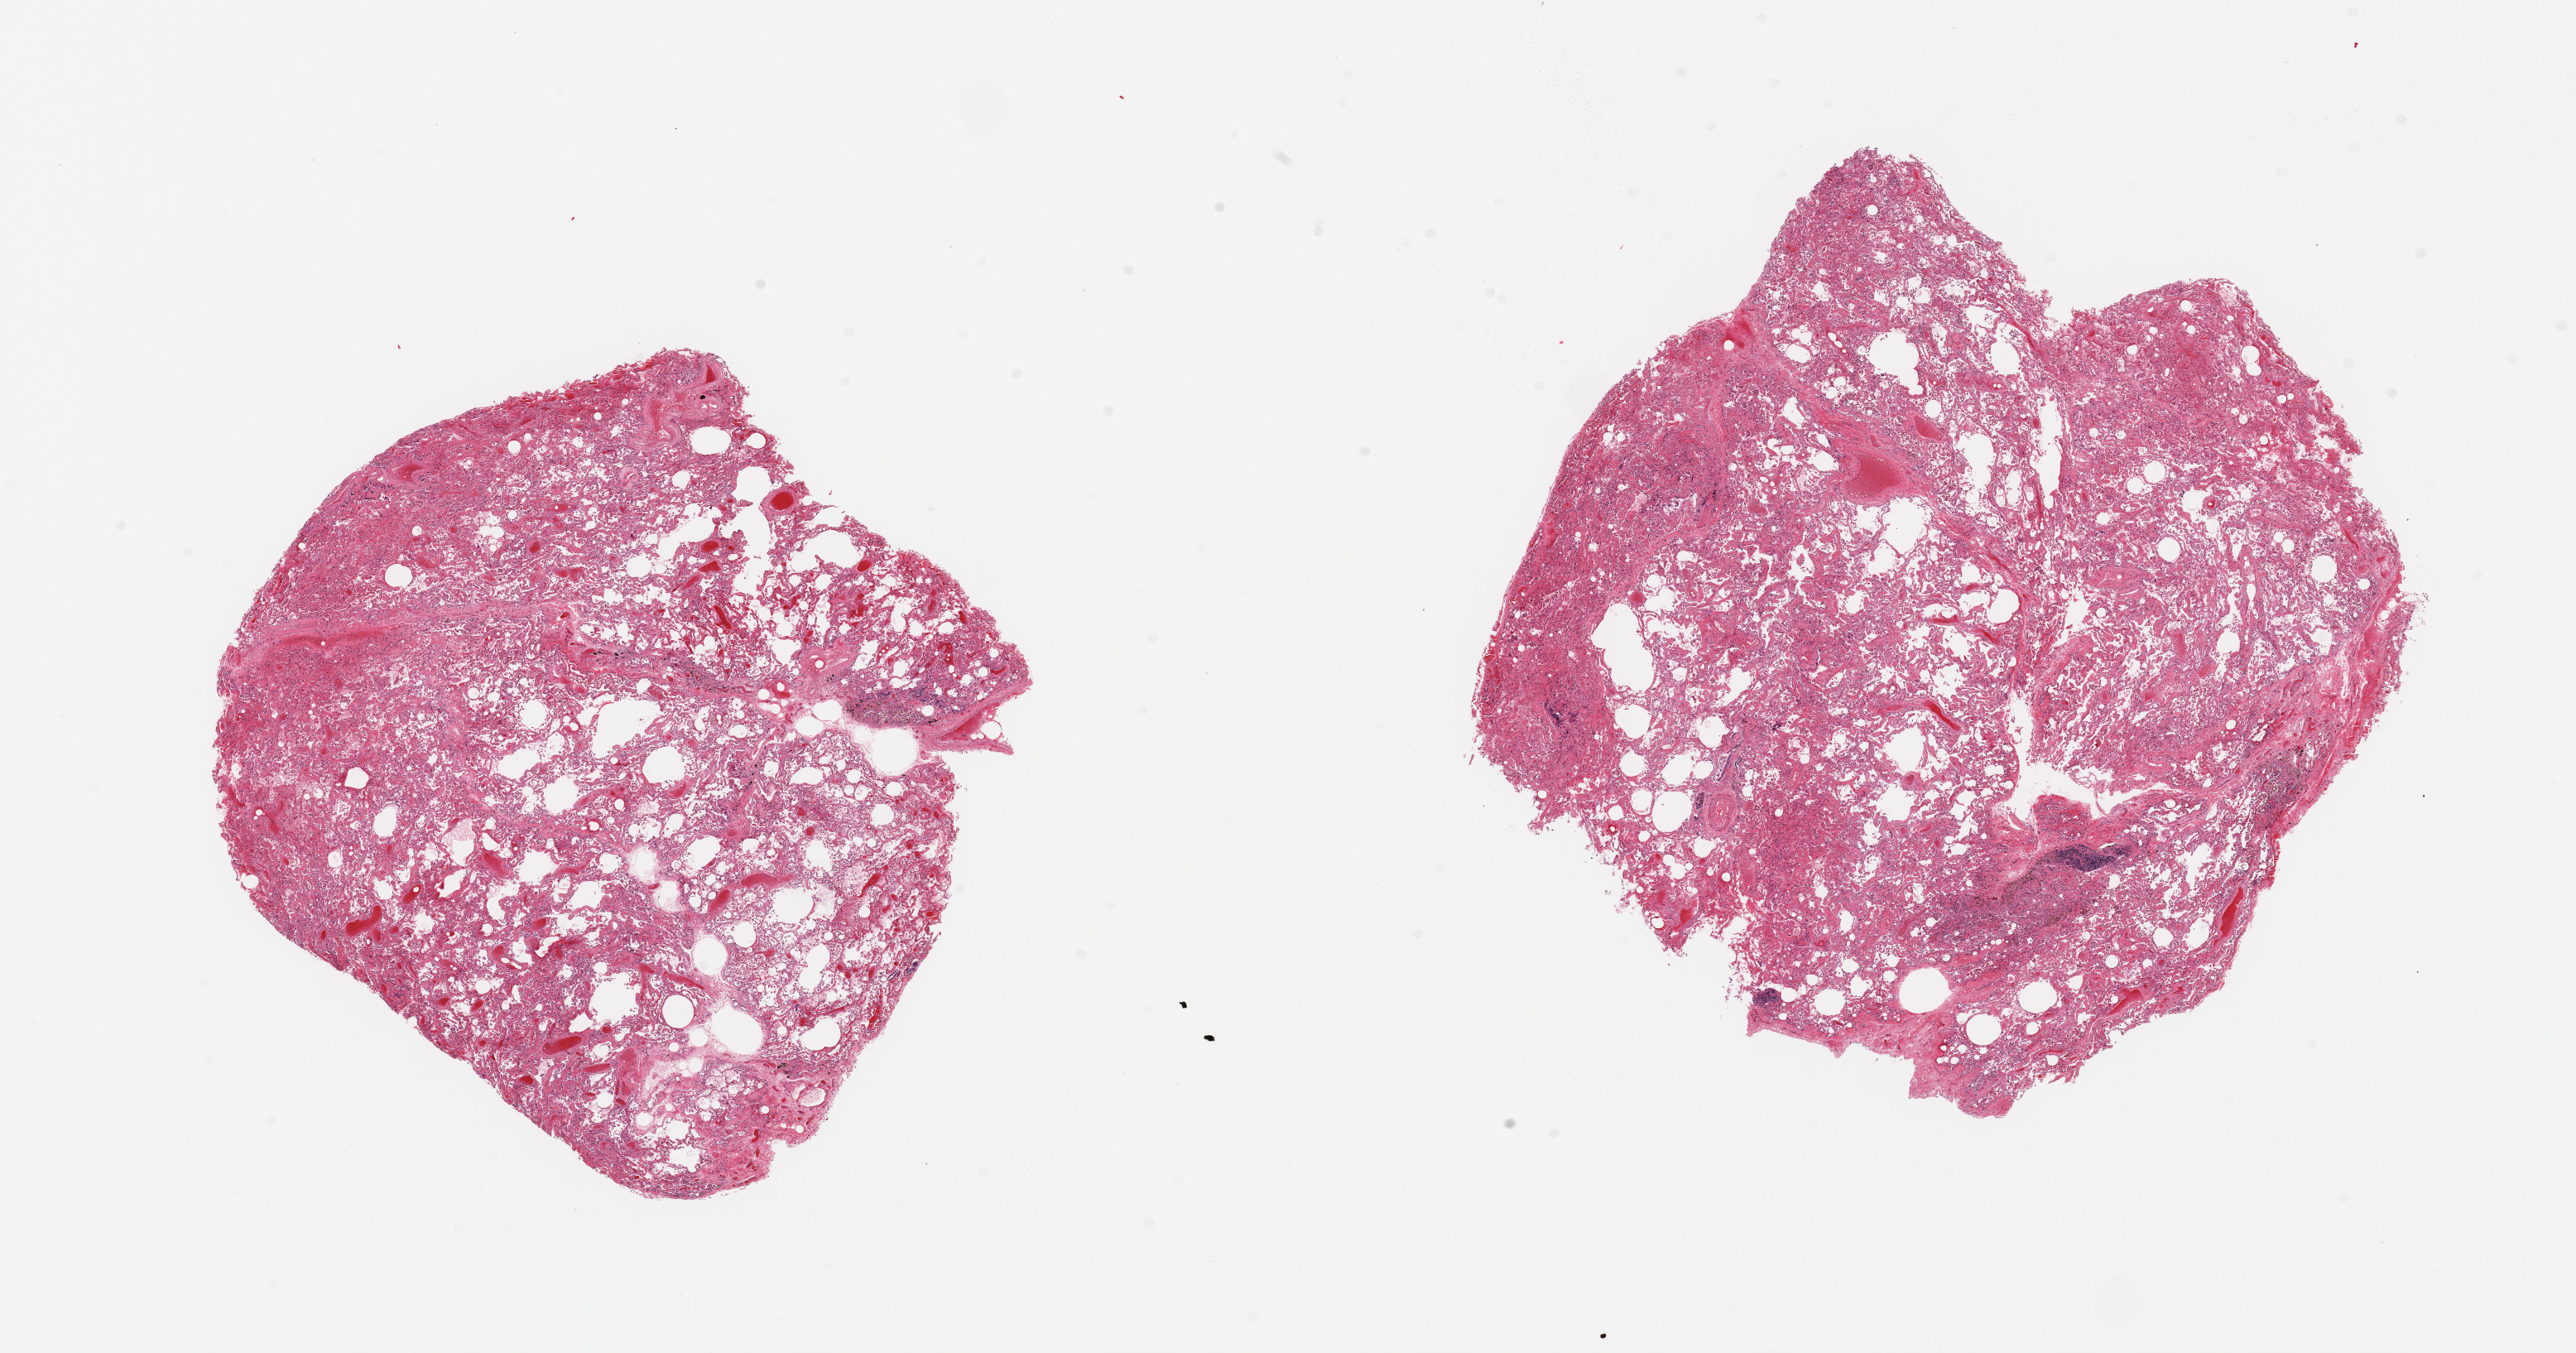
Whole-slide image, haematoxylin and eosin stain, low-resolution overview of the scanned area, about 24.6 x 12.9 mm (slide scanned at 20x). PAXgene-fixed, paraffin-embedded tissue. Section of lung (target tissue). Donor tissue sample. Donor: female.
Pathologist's review note for this sample: 2 pieces; pigmented alveolar macrophages, patchy interstitial fibrosis; focal alveolar hemorrhage.